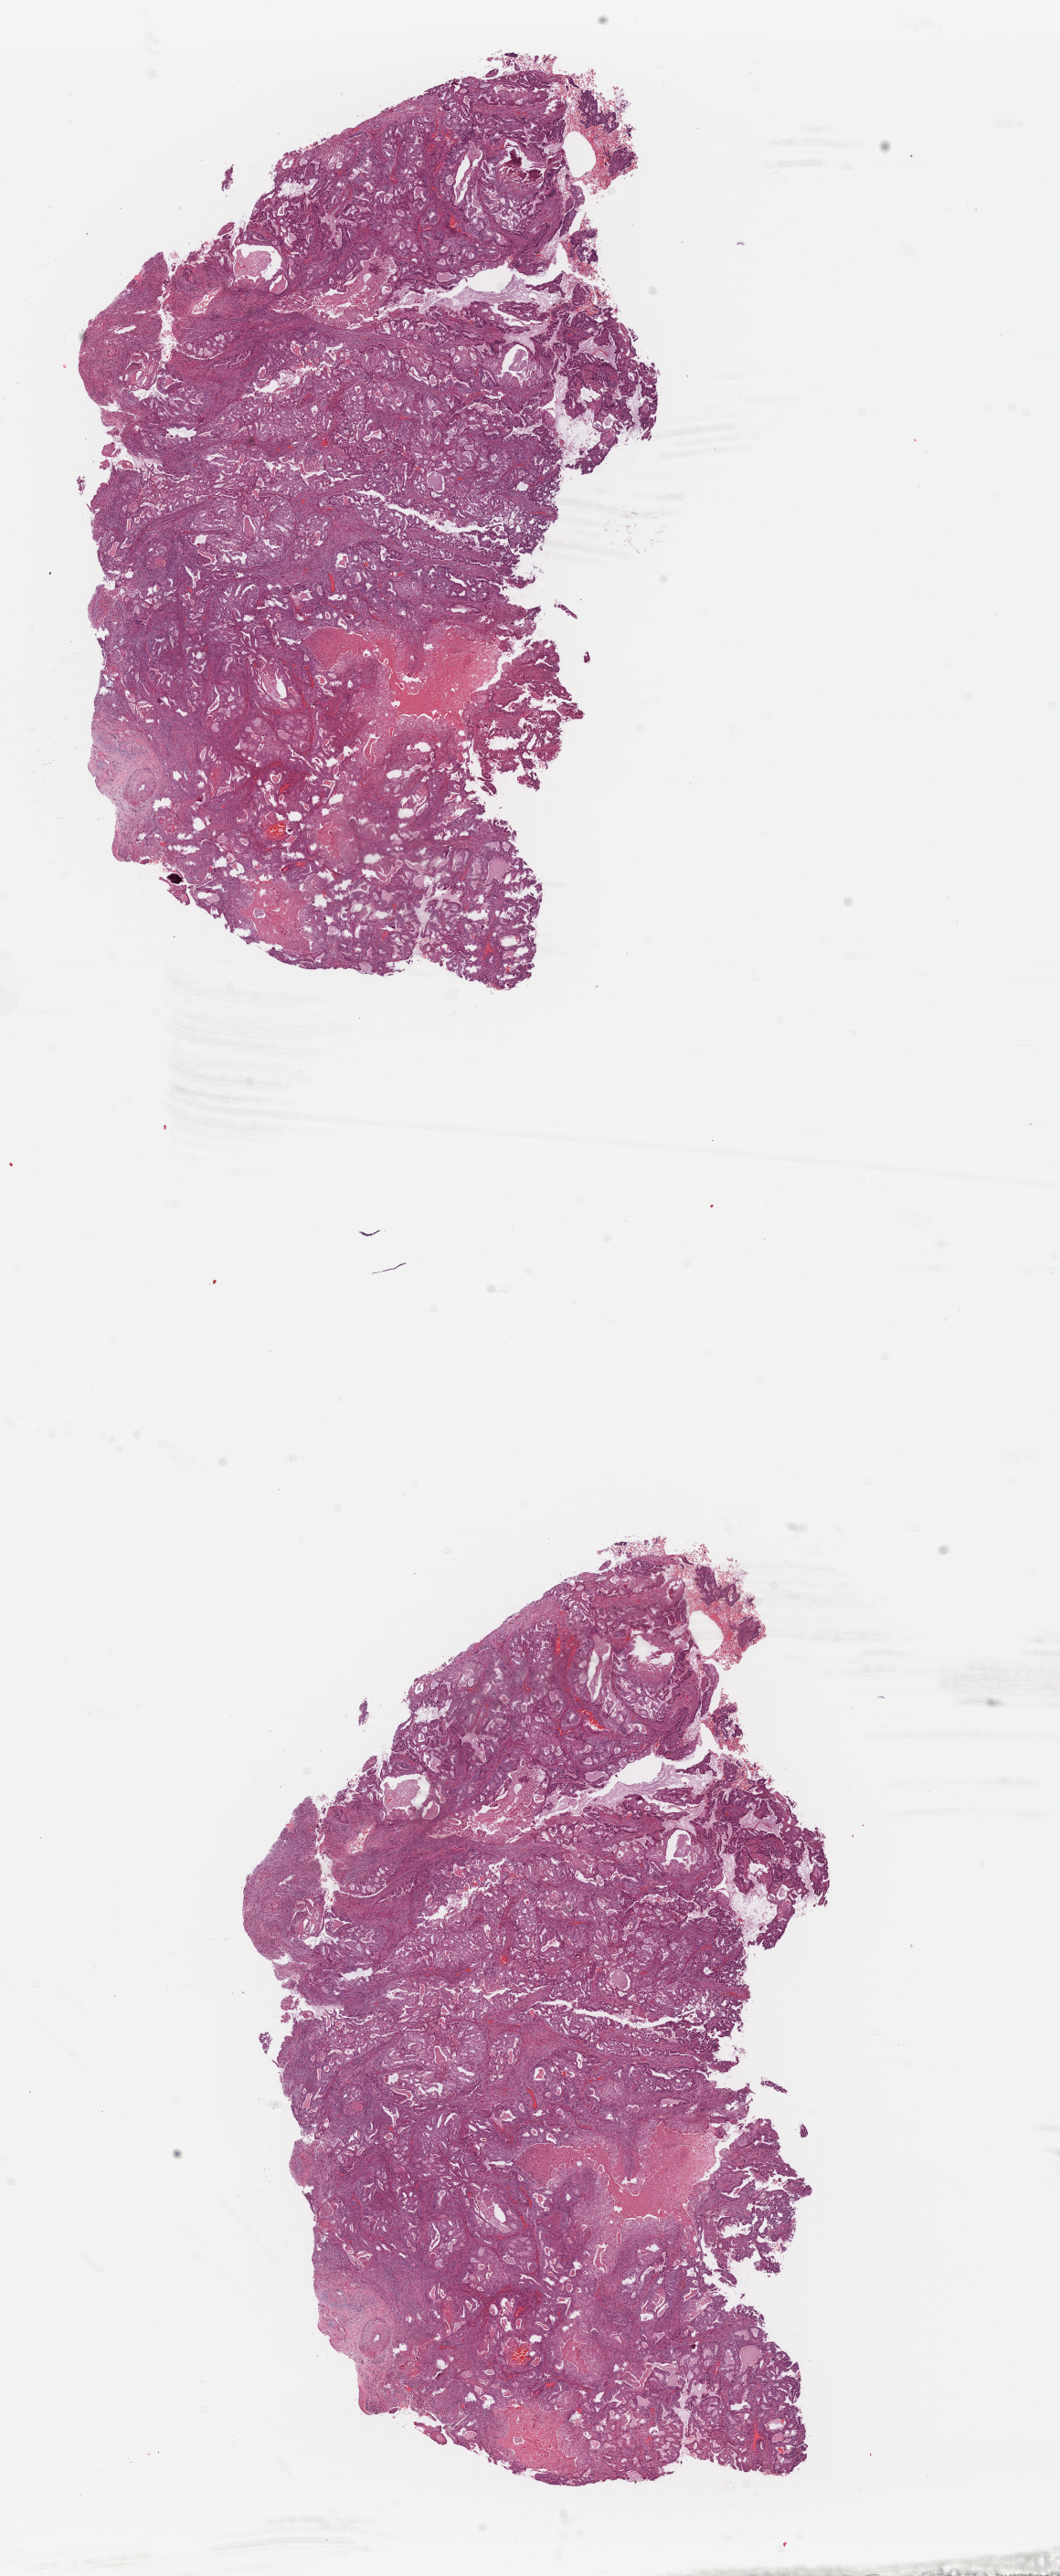
Digitized H&E tissue section (whole slide) — shown as a low-resolution overview of the whole scanned area (about 9.2 x 22.2 mm), formalin-fixed paraffin-embedded (FFPE) diagnostic section, primary tumour sample from the uterus. Female patient; age at initial diagnosis 60 years.
Histologic diagnosis: Endometrioid adenocarcinoma, NOS (endometrium).